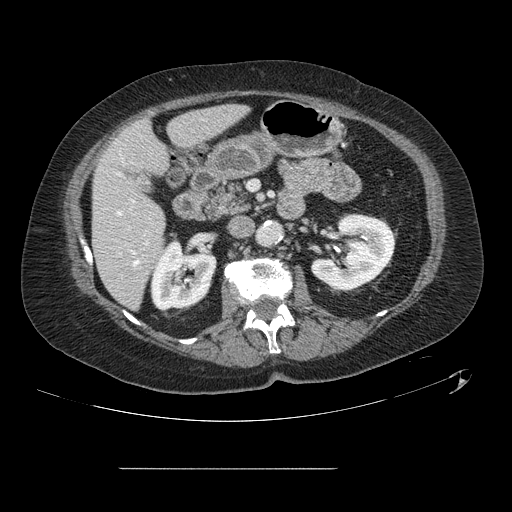
Contrast-enhanced abdominal CT, one axial slice. Position 50 of 148 along the scan axis. 120 kVp. Intravenous contrast given. Soft-tissue window (W 400 / L 40 HU). 512 × 512 image matrix. Female patient, age 75 years. Case-level facts recorded for this patient, not image findings: diagnosis: colorectal cancer liver metastases, imaged before liver resection; multiple liver metastases: no; largest metastasis: 2.4 cm; disease in both lobes: no.
Annotated regions visible in this slice (expert manual segmentation):
- hepatic veins: bounding box [x1, y1, x2, y2] px = [118, 212, 139, 265]
- liver: [93, 105, 245, 308]
- planned liver remnant (the part of the liver to remain after resection): [93, 105, 245, 308]